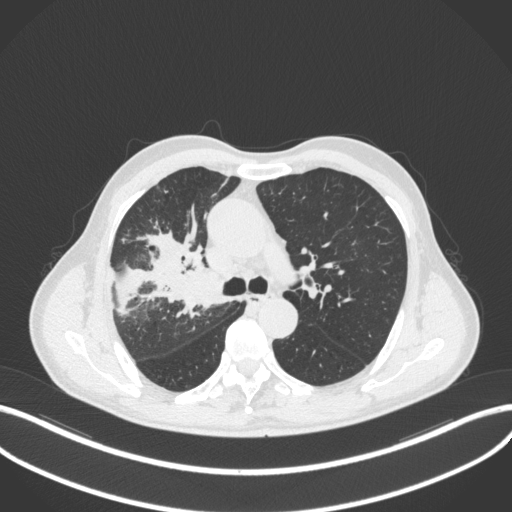
Chest CT, one axial slice. Position 322 of 490 along the scan axis. Reconstruction kernel B31f. 120 kVp. Lung window (W 1500 / L -600 HU). 1 mm slice thickness. 512 × 512 image matrix. Male patient, age 69 years. Case-level facts recorded for this patient, not image findings: clinical TNM (as recorded): T2a N0 M0.
Structures marked on this image (bounding box drawn by a radiologist):
- lung tumour (recorded histology: adenocarcinoma): box from (x=164, y=263) to (x=216, y=310) px